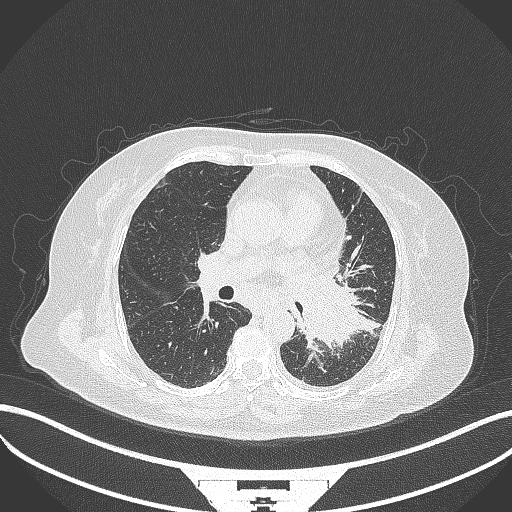
Chest CT, one axial slice; slice 188 of 322 in the series (ordered by position); 120 kVp; lung window (W 1500 / L -600 HU); 1 mm slice thickness; 512 × 512 image matrix, field of view 400 × 400 mm. Patient: female, 69 years. From the clinical record (not read from this slice): clinical TNM (as recorded): T2b N3 M1.
Outlined on this slice (rectangle marked by the reading radiologist):
- lung tumour (recorded histology: adenocarcinoma): bounding box <300,280,365,349> (left, top, right, bottom; pixels)